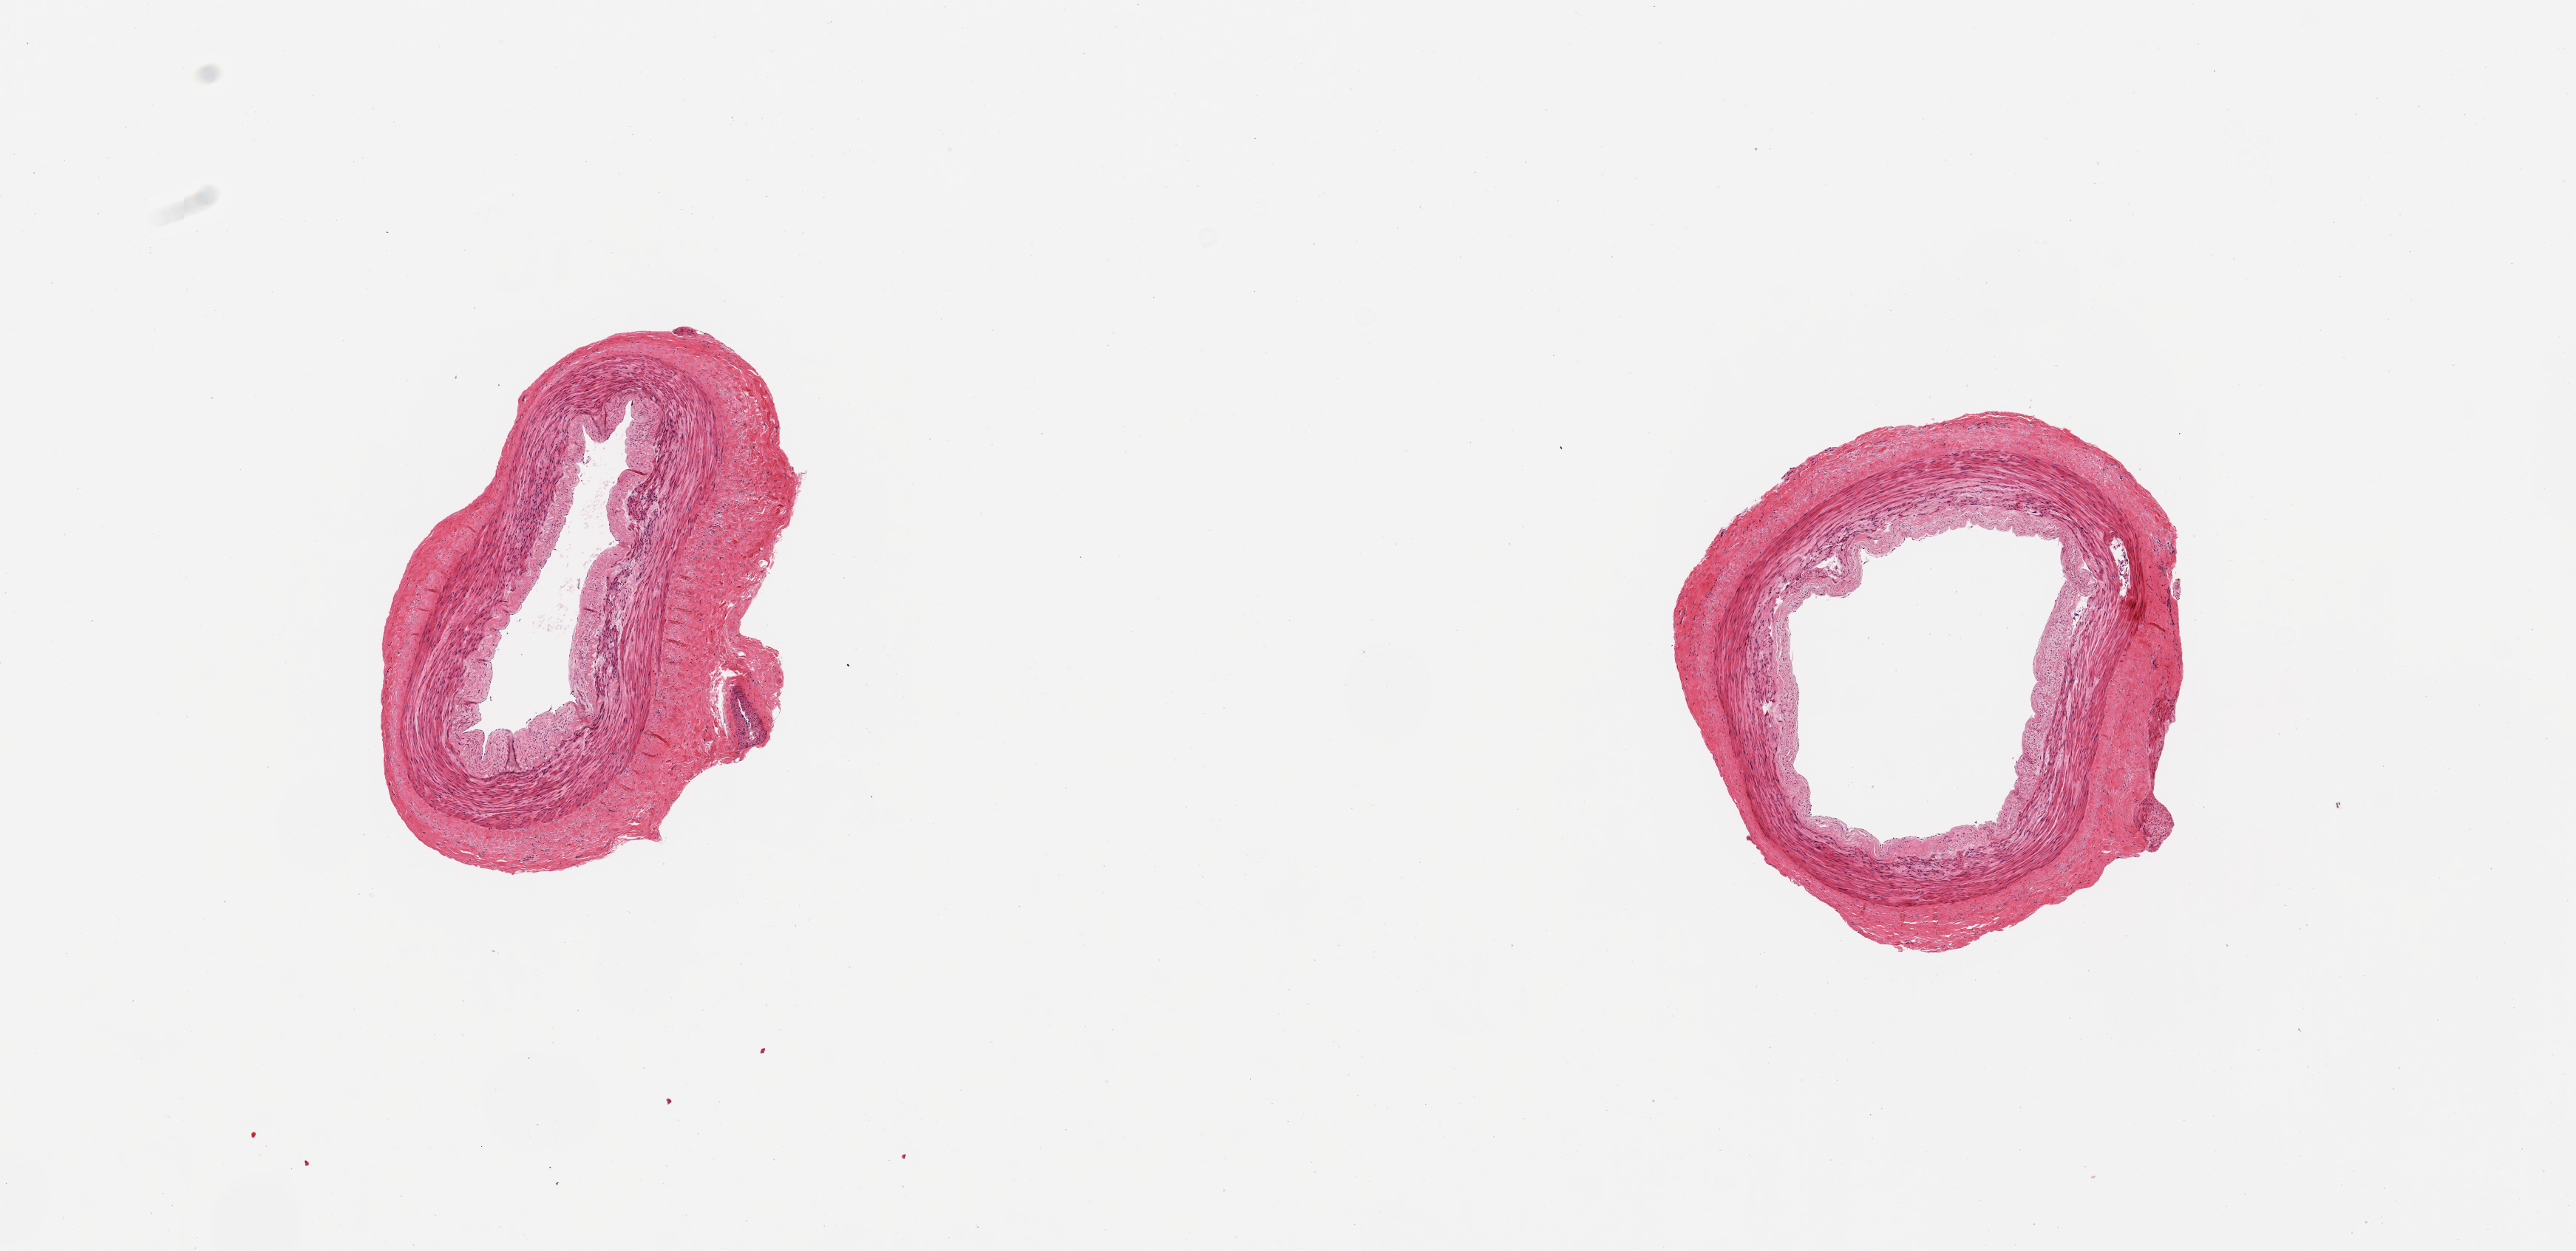
Haematoxylin and eosin whole-slide image, shown as a low-resolution overview of the whole scanned area (about 13.8 x 6.7 mm); PAXgene-fixed paraffin-embedded (PFPE) section; target tissue: tibial artery; donor tissue sample. Female donor.
Review note (as recorded): 2 pieces.